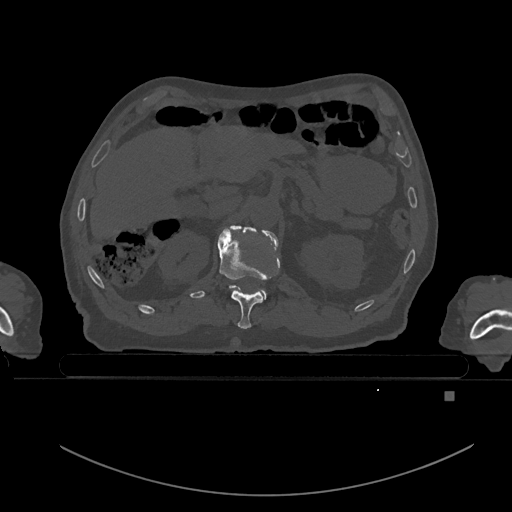
CT including the spine, one axial slice; slice 5 of 969 in the series (ordered by position); bone window (W 1800 / L 400 HU); 0.5 mm slice thickness; 512 × 512 image matrix. Male patient, age 82 years. Case-level facts recorded for this patient, not image findings: primary cancer: prostate.
Annotated regions visible in this slice (semi-automatic segmentation, software-assisted and operator-edited):
- T11 vertebra: bounding box (x1, y1, x2, y2) in pixels: (218, 227, 280, 329)